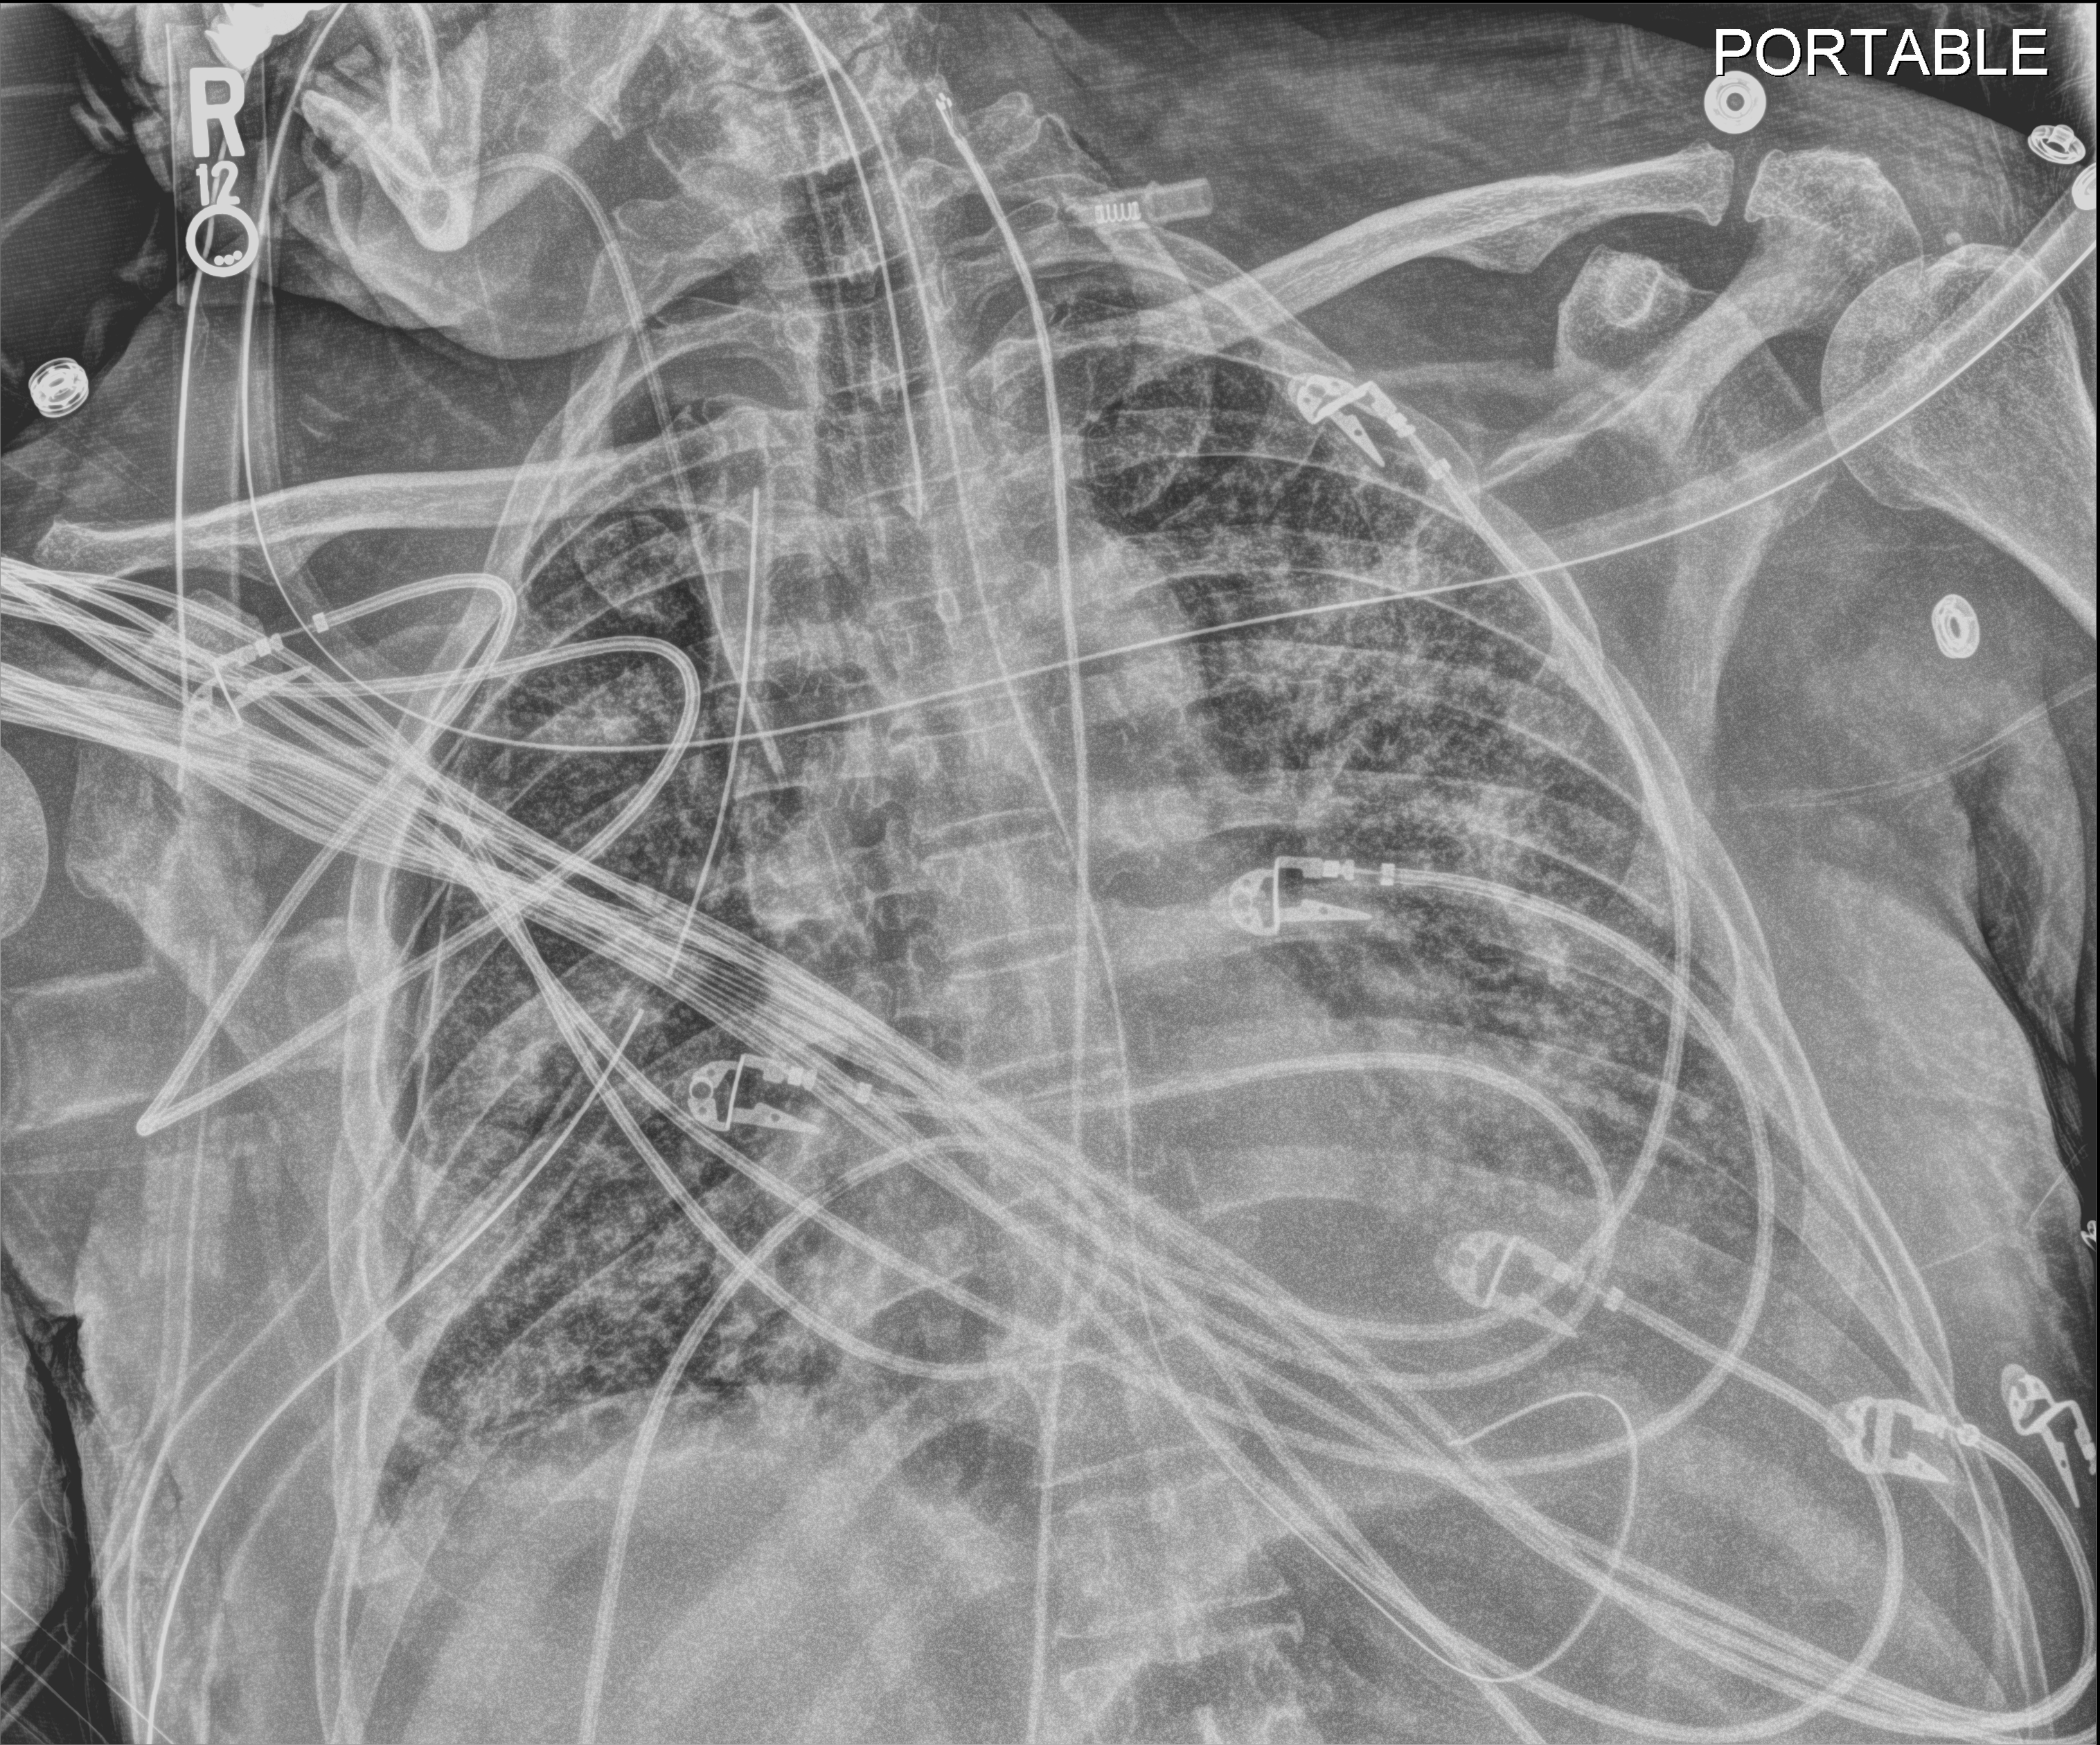
Portable chest radiograph; anteroposterior (AP) projection. Male patient hospitalised with COVID-19, age 60–74 years.
From the hospital-stay record, not from the radiograph (when in the stay this image was taken is not recorded):
- other chronic lung disease (admission record): no
- mechanically ventilated during this hospital stay: yes